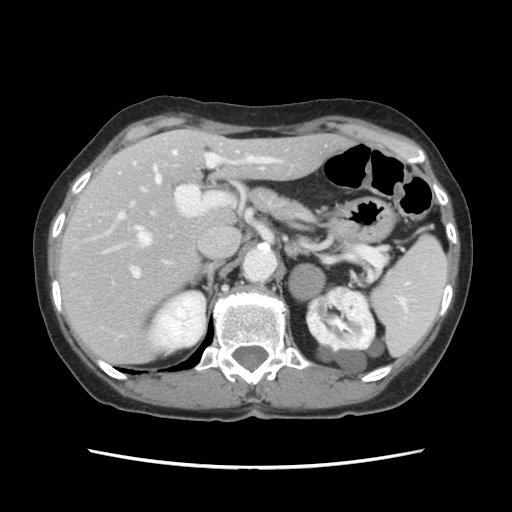
Contrast-enhanced abdominal CT, one axial slice. Position 81 of 120 along the scan axis. Intravenous contrast given. Soft-tissue window (W 400 / L 40 HU). 2.5 mm slice thickness. 512 × 512 image matrix, field of view 330 × 330 mm. Female patient, age 70 years. Case-level facts recorded for this patient, not image findings: diagnosis: colorectal cancer liver metastases, imaged before liver resection; multiple liver metastases: no; largest metastasis: 2.5 cm; chemotherapy before resection: yes.
Structures marked on this image (outlined manually by an expert reader):
- hepatic veins: box from (x=136, y=151) to (x=177, y=245) px
- liver: (x=60, y=130)–(x=342, y=363)
- planned liver remnant (the part of the liver to remain after resection): (x=99, y=130)–(x=343, y=287)
- portal vein (with intrahepatic branches): (x=118, y=154)–(x=282, y=277)